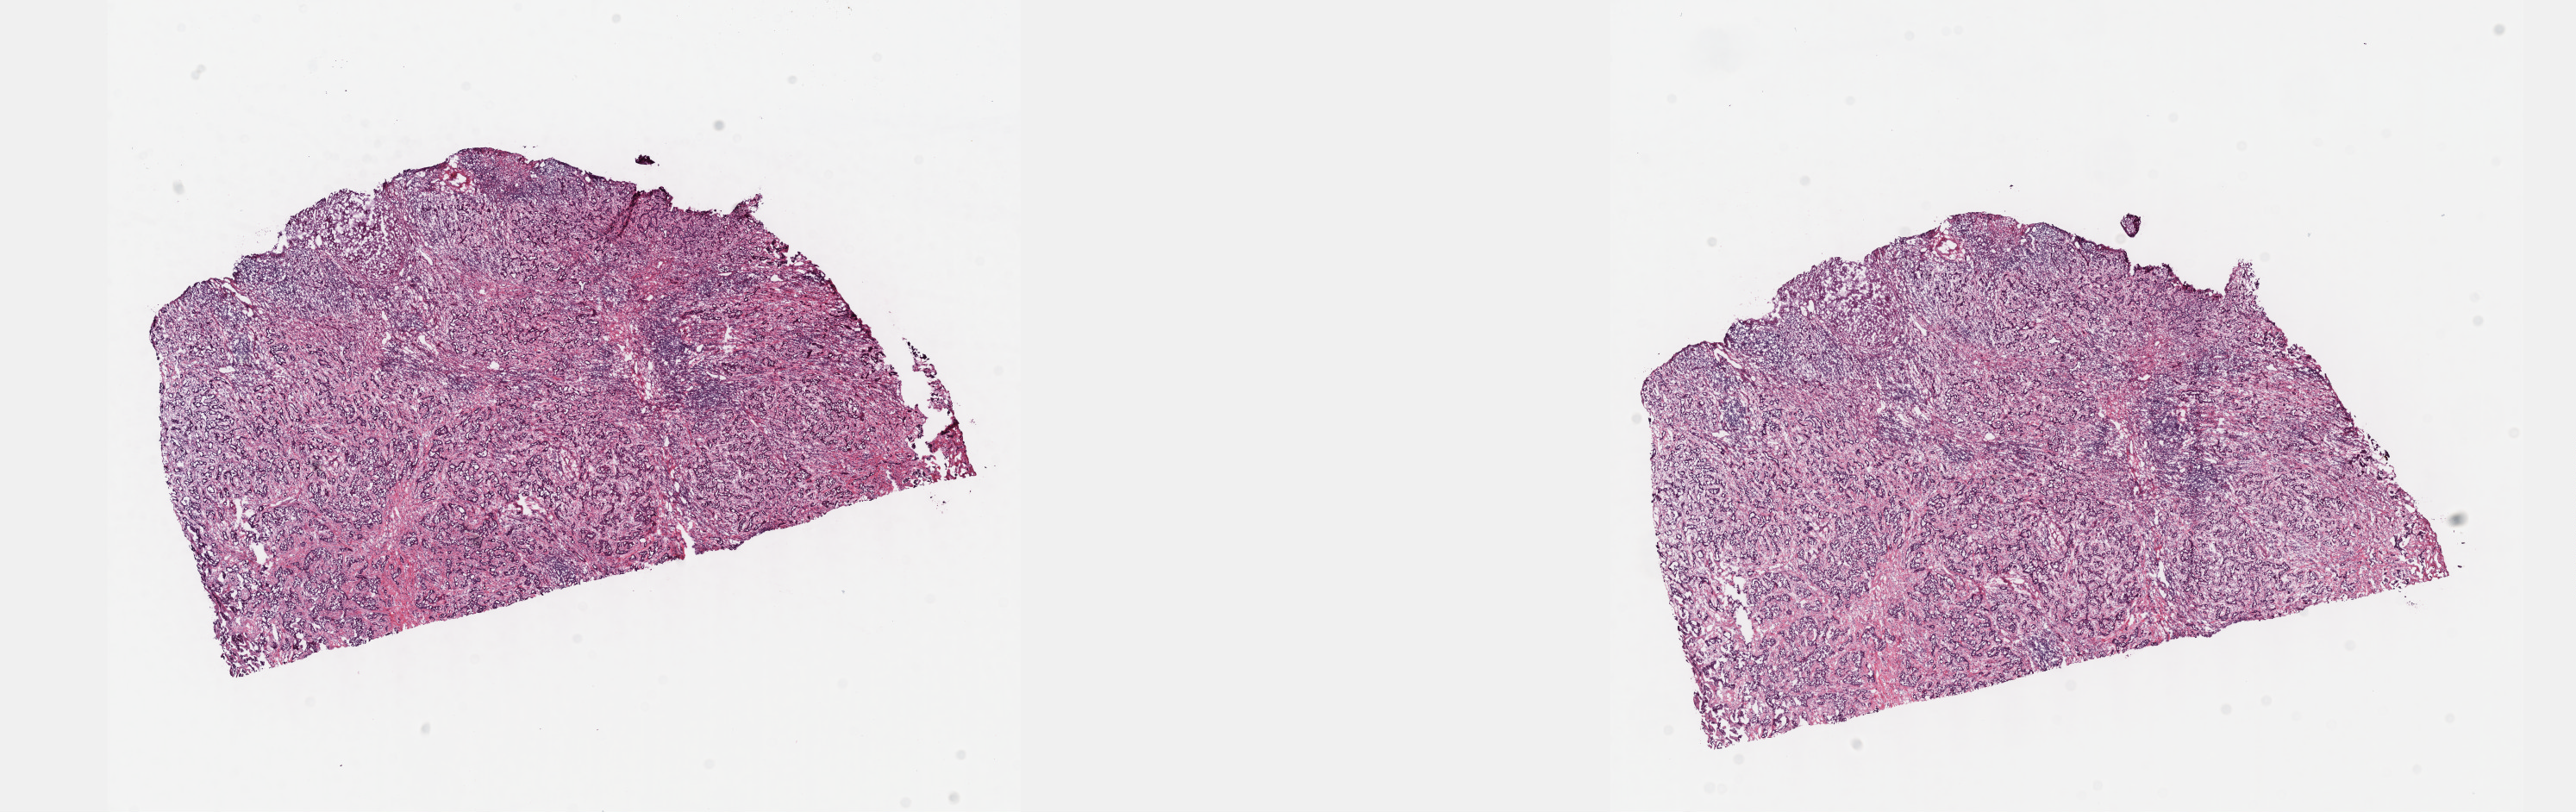
Digitized H&E-stained tissue section (whole slide), low-resolution overview of the scanned area, about 24.1 x 7.6 mm (acquisition: 40x scan). Frozen section. Bile duct, primary tumour sample. Patient: female, age at initial diagnosis 71 years. Histologic grade: G2 (moderately differentiated). Composition of this section per pathologist review: tumour cells 56%, tumour nuclei 80%, normal cells 4%, stromal cells 39%, necrosis 1%. Infiltration values recorded for this section: lymphocyte infiltration 15%, monocyte infiltration 1%, neutrophil infiltration 1%.
Histologic diagnosis: Cholangiocarcinoma (liver). AJCC pathologic stage: II (7th edition). TNM: T2b NX MX.